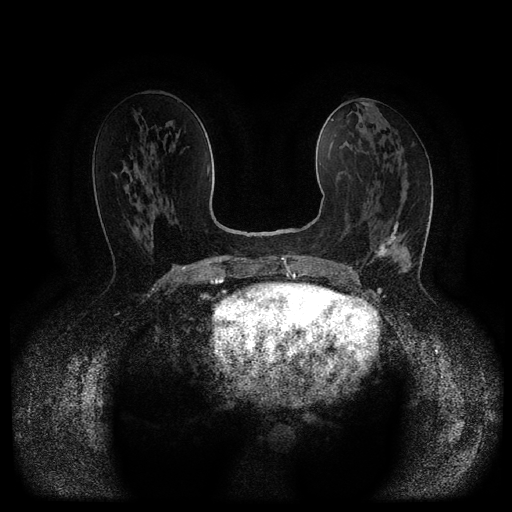
Breast MRI (dynamic contrast-enhanced, multi-phase), one axial slice; dynamic contrast-enhanced series, time point 2 of 5 at this slice position (early post-contrast); 1.5 T; TE 2.6 ms, TR 5.4 ms; 512 × 512 image matrix, field of view 340 × 340 mm. Patient: female, 61 years.
Annotated regions visible in this slice (semi-automatic segmentation, software-assisted and operator-edited):
- breast lesion (labelled 'tumour' in the annotation; benign lesions carry a separate 'benign' label): bounding box [x1, y1, x2, y2] px = [376, 222, 399, 258]